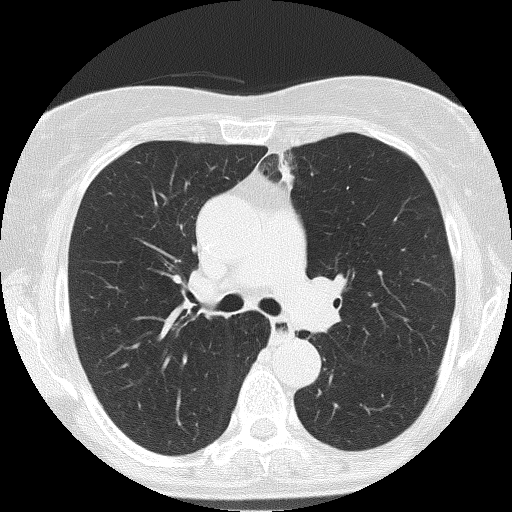
Low-dose screening chest CT, one axial slice. Position 110 of 166 along the scan axis. 120 kVp. Lung window (W 1500 / L -600 HU). 512 × 512 image matrix, field of view 303 × 303 mm.
Outlined on this slice (manually delineated by an expert):
- lesion 2 (nodule, upper lobe of left lung): box from (x=279, y=156) to (x=293, y=184) px